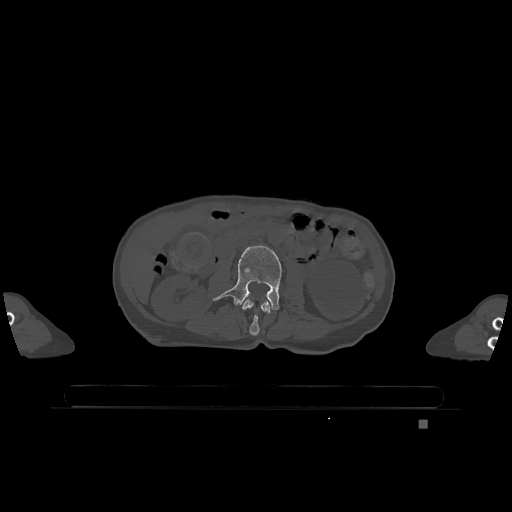
CT including the spine, one axial slice. Slice 374 of 1317 in the series (ordered by position). Bone window (W 1800 / L 400 HU). 512 × 512 image matrix, field of view 500 × 500 mm. Female patient, age 74 years. From the clinical record (not read from this slice): primary cancer: lung; vertebrae with lytic lesions (as recorded): T1, T4, T5, T6, L4, L5.
Annotated regions visible in this slice (semi-automatic segmentation, software-assisted and operator-edited):
- L2 vertebra: box from (x=242, y=299) to (x=272, y=336) px
- L3 vertebra: (x=213, y=245)–(x=282, y=310)